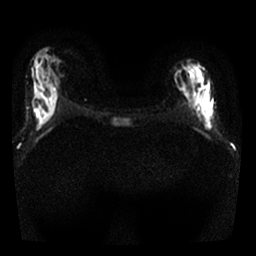
Breast MRI, one axial slice; diffusion-weighted series; image 2 of 4 stored at this slice position (different b-values; order by instance number); 1.5 T; 4 mm slice thickness; 256 × 256 image matrix. Female patient.
Structures marked on this image (expert manual segmentation):
- tumour on diffusion-weighted imaging: bounding box <180,80,214,132> (left, top, right, bottom; pixels)